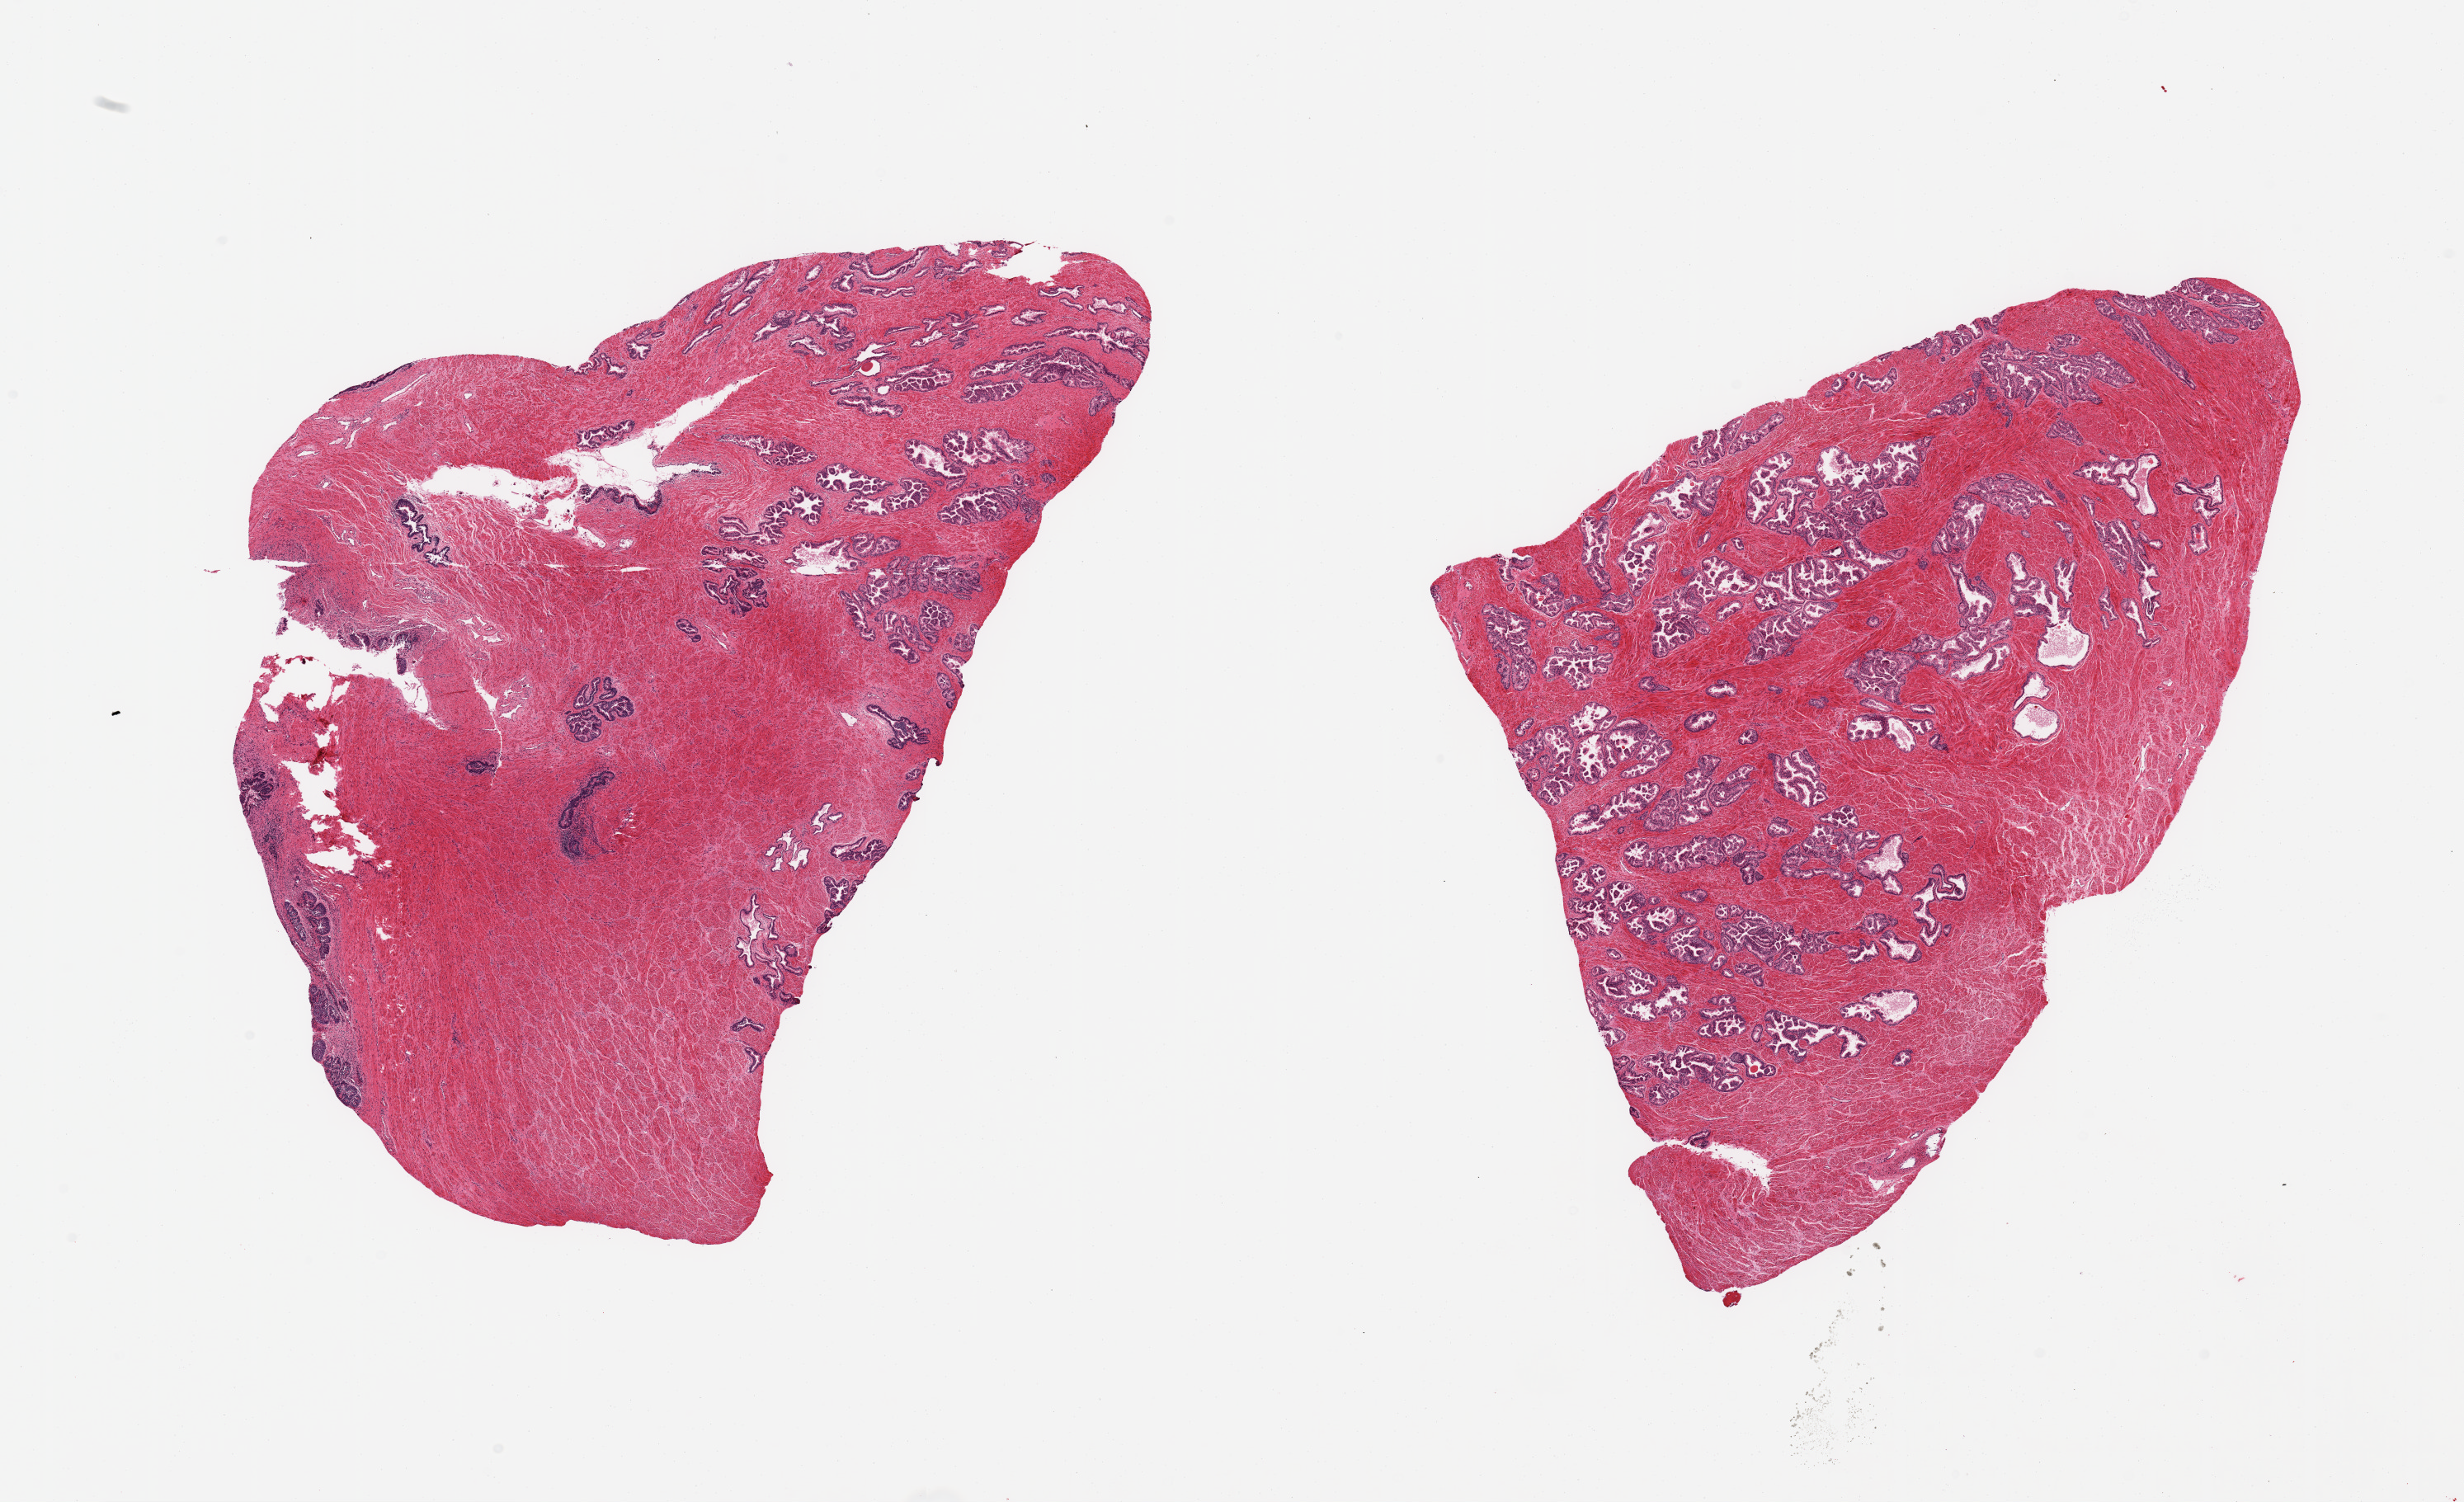
H&E whole-slide image, brightfield, a low-resolution overview of the entire scanned area, about 23.6 x 14.4 mm. PAXgene-fixed paraffin-embedded (PFPE) section. Target tissue: prostate. Donor tissue sample. Male donor.
Reviewer comment on this tissue sample: 2 pieces; one piece includes portion of prostatic urethra.